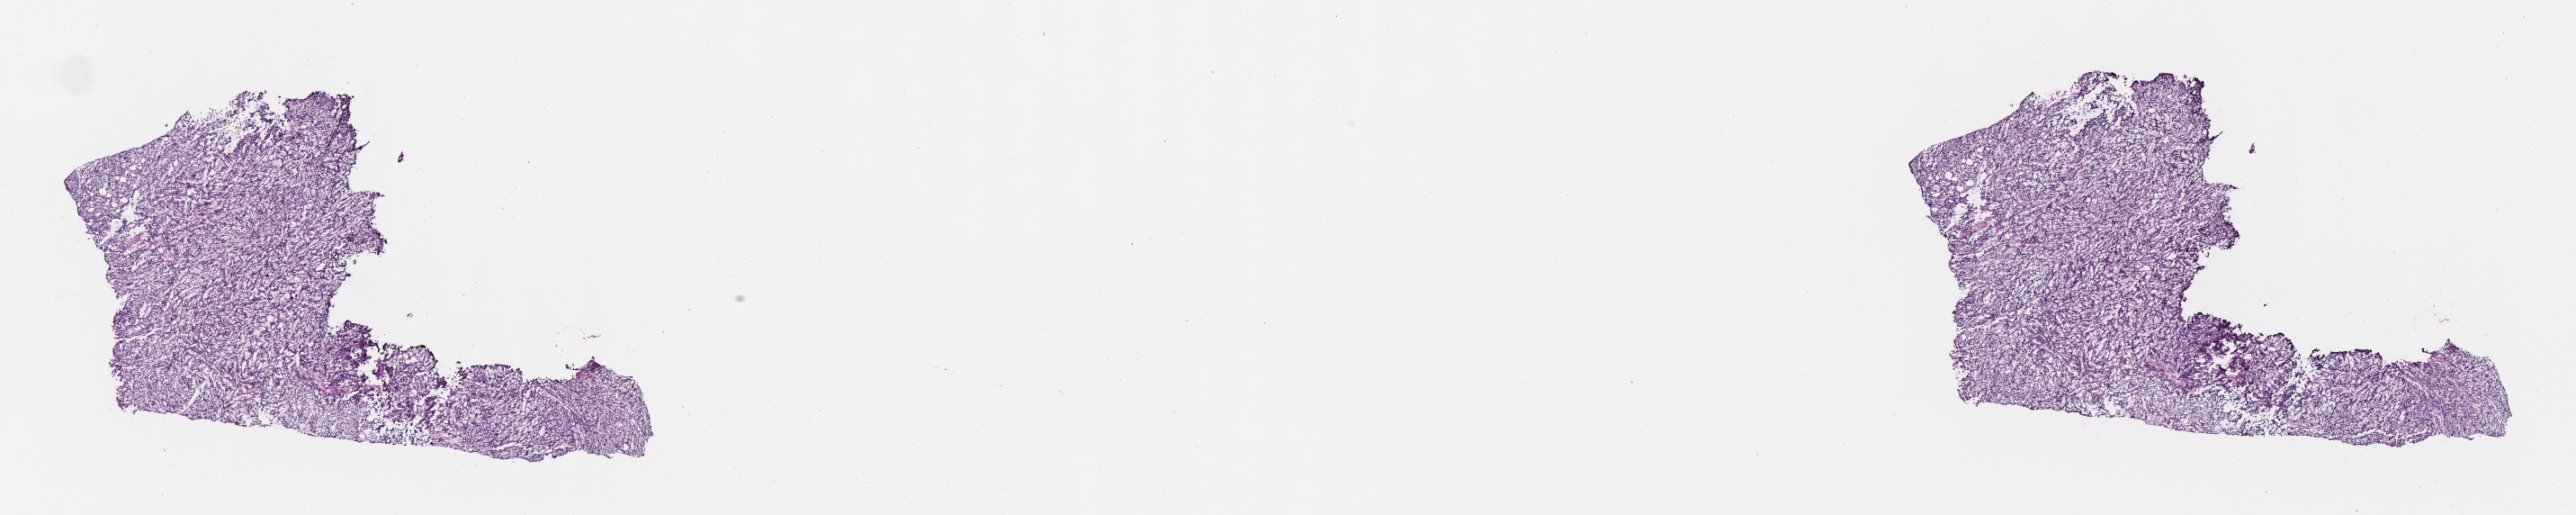
Digitized hematoxylin and eosin (H&E)-stained section, low-resolution overview of the scanned area, about 23.1 x 4.6 mm. Frozen section (tissue freezing medium). Primary tumor. Anatomic site: upper lobe of right lung. Patient male; age 40 years. Slide review estimates, as recorded: tumor cells 75%, tumor nuclei 75%, stromal cells 24%, necrosis 1%, normal cells 0%. Infiltration values recorded for this section: lymphocyte infiltration 4%, monocyte infiltration 3%, neutrophil infiltration 5%.
- histologic diagnosis: Adenocarcinoma, NOS
- section: top of the tissue portion
- AJCC pathologic stage: Stage IIIA